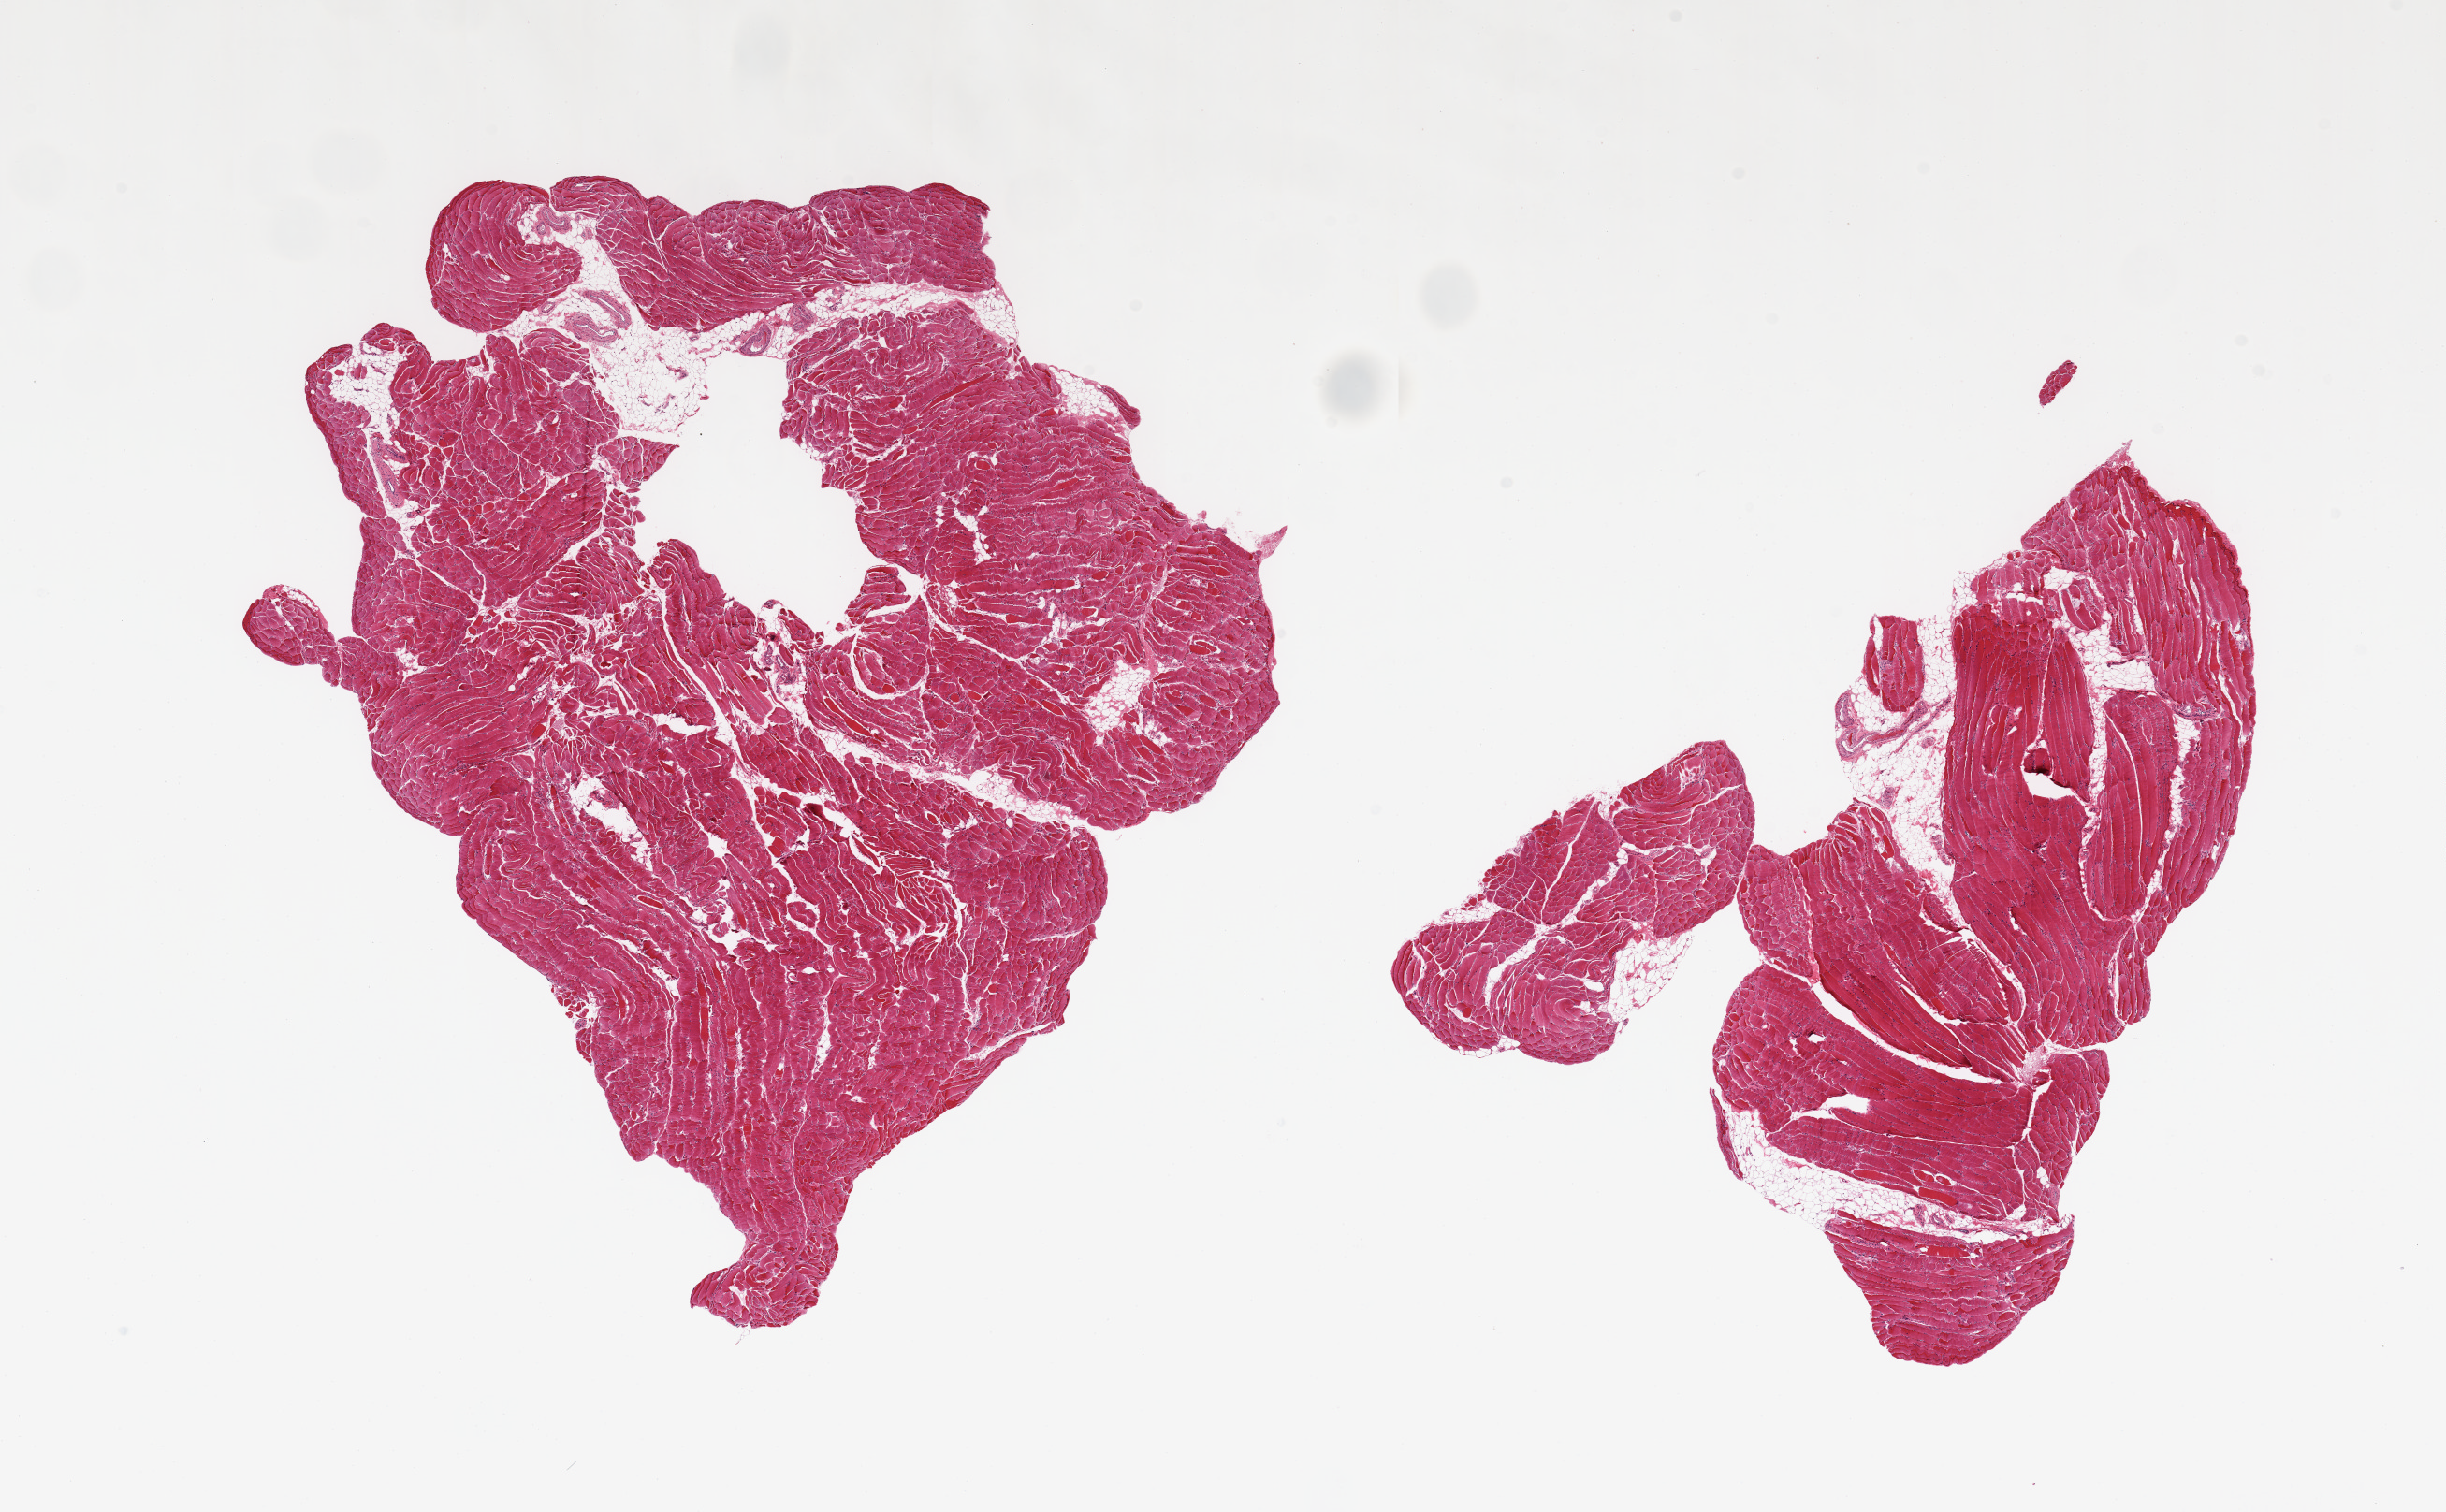
Digitized hematoxylin and eosin (H&E)-stained section — shown as a low-resolution overview of the whole scanned area (about 20.7 x 12.8 mm, acquisition: 20x scan), PAXgene-fixed, paraffin-embedded tissue, section of skeletal muscle (target tissue), donor tissue sample. Donor sex: female.
Review note (as recorded): 2 pieces, ~10% interstitial fat/vascular elements.